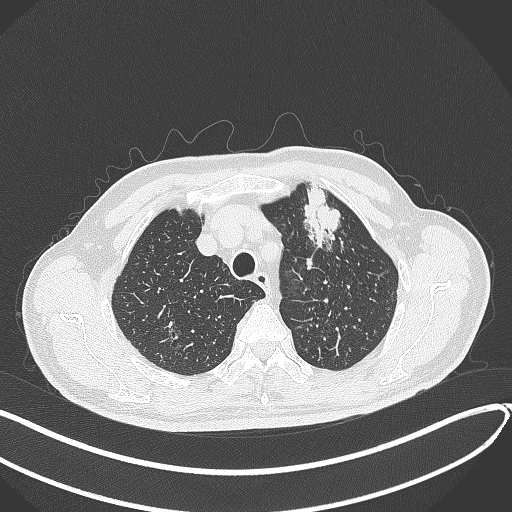
Chest CT, one axial slice. Slice 344 of 459 in the series (ordered by position). Reconstruction kernel B70f. 120 kVp. Lung window (W 1500 / L -600 HU). 512 × 512 image matrix, field of view 400 × 400 mm. Patient: male, 74 years. From the clinical record (not read from this slice): clinical TNM (as recorded): T2b N0 M1c.
Structures marked on this image (bounding box drawn by a radiologist):
- lung tumour (recorded histology: adenocarcinoma): box from (x=294, y=181) to (x=349, y=257) px